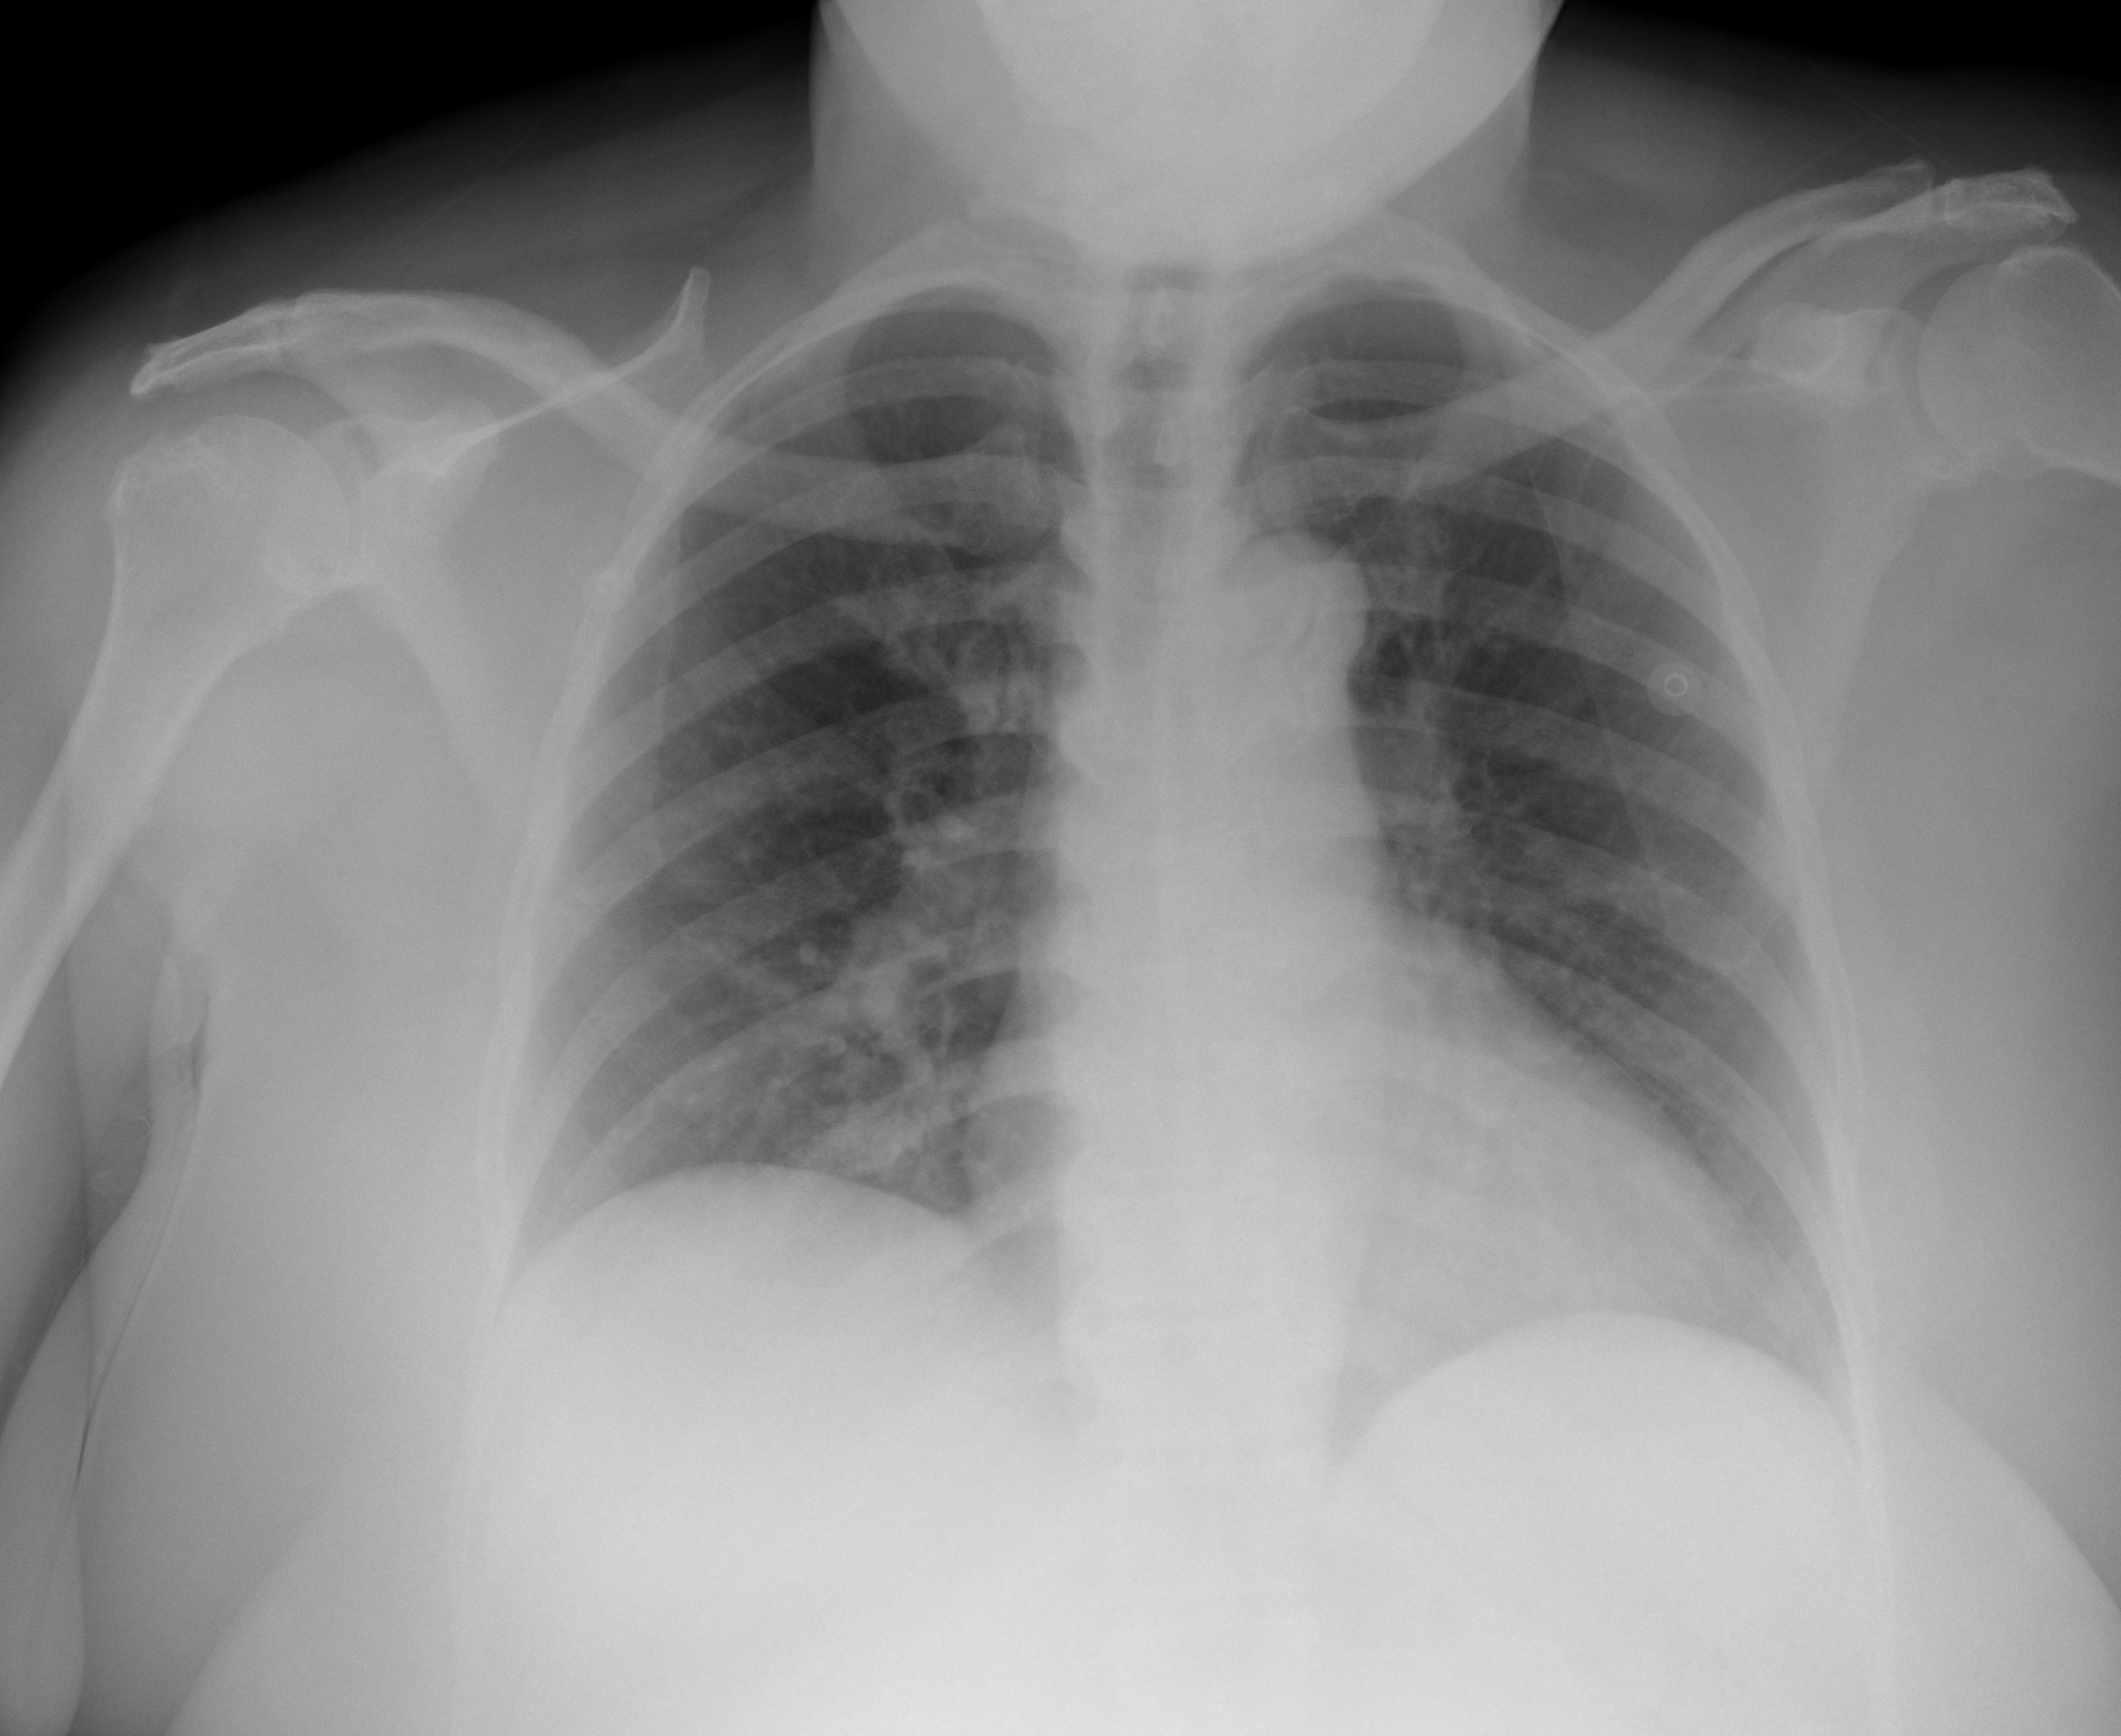
Portable chest radiograph, AP projection. Female patient, age 61 years; imaged 0 days after the COVID-19 diagnosis.
Radiologist's key findings for this exam: No relevant findings.